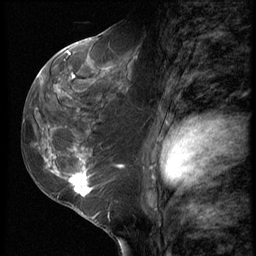
Breast MRI (dynamic contrast-enhanced), one sagittal slice. Slice 33 of 62 in the series (ordered by position). 3 images stored at this slice position (order not interpretable as contrast timing). 1.5 T. TE 4.2 ms, TR 9 ms. 2.5 mm slice thickness. 256 × 256 image matrix, field of view 180 × 180 mm. Female patient, age 50 years. Case-level facts recorded for this patient, not image findings: setting: breast cancer imaged before/during neoadjuvant chemotherapy; receptor status: HR-positive, HER2-negative.
Annotated regions visible in this slice (semi-automatic segmentation, software-assisted and operator-edited):
- analysis volume of interest (the breast-tissue region the enhancement analysis was run in; not a lesion): bounding box <32,91,118,209> (left, top, right, bottom; pixels)
- tumour enhancement mask (voxels above the 140 % enhancement threshold inside the analysis volume of interest): <45,153,94,195>